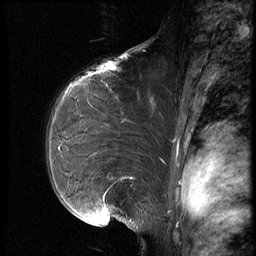
Breast MRI (dynamic contrast-enhanced), one sagittal slice; slice 46 of 66 in the series (ordered by position); dynamic contrast-enhanced series, image 2 of 3 at this slice position (ordered by acquisition); 1.5 T; TE 4.2 ms, TR 8.9 ms; 2.5 mm slice thickness; 256 × 256 image matrix, field of view 200 × 200 mm. Female patient, age 39 years. Case-level facts recorded for this patient, not image findings: setting: breast cancer imaged before/during neoadjuvant chemotherapy; receptor status: HER2-positive.
Annotated regions visible in this slice (semi-automatically segmented with operator editing):
- analysis volume of interest (the breast-tissue region the enhancement analysis was run in; not a lesion): bounding box [x1, y1, x2, y2] px = [43, 75, 171, 218]
- tumour enhancement mask (voxels above the 140 % enhancement threshold inside the analysis volume of interest): [106, 86, 112, 181]